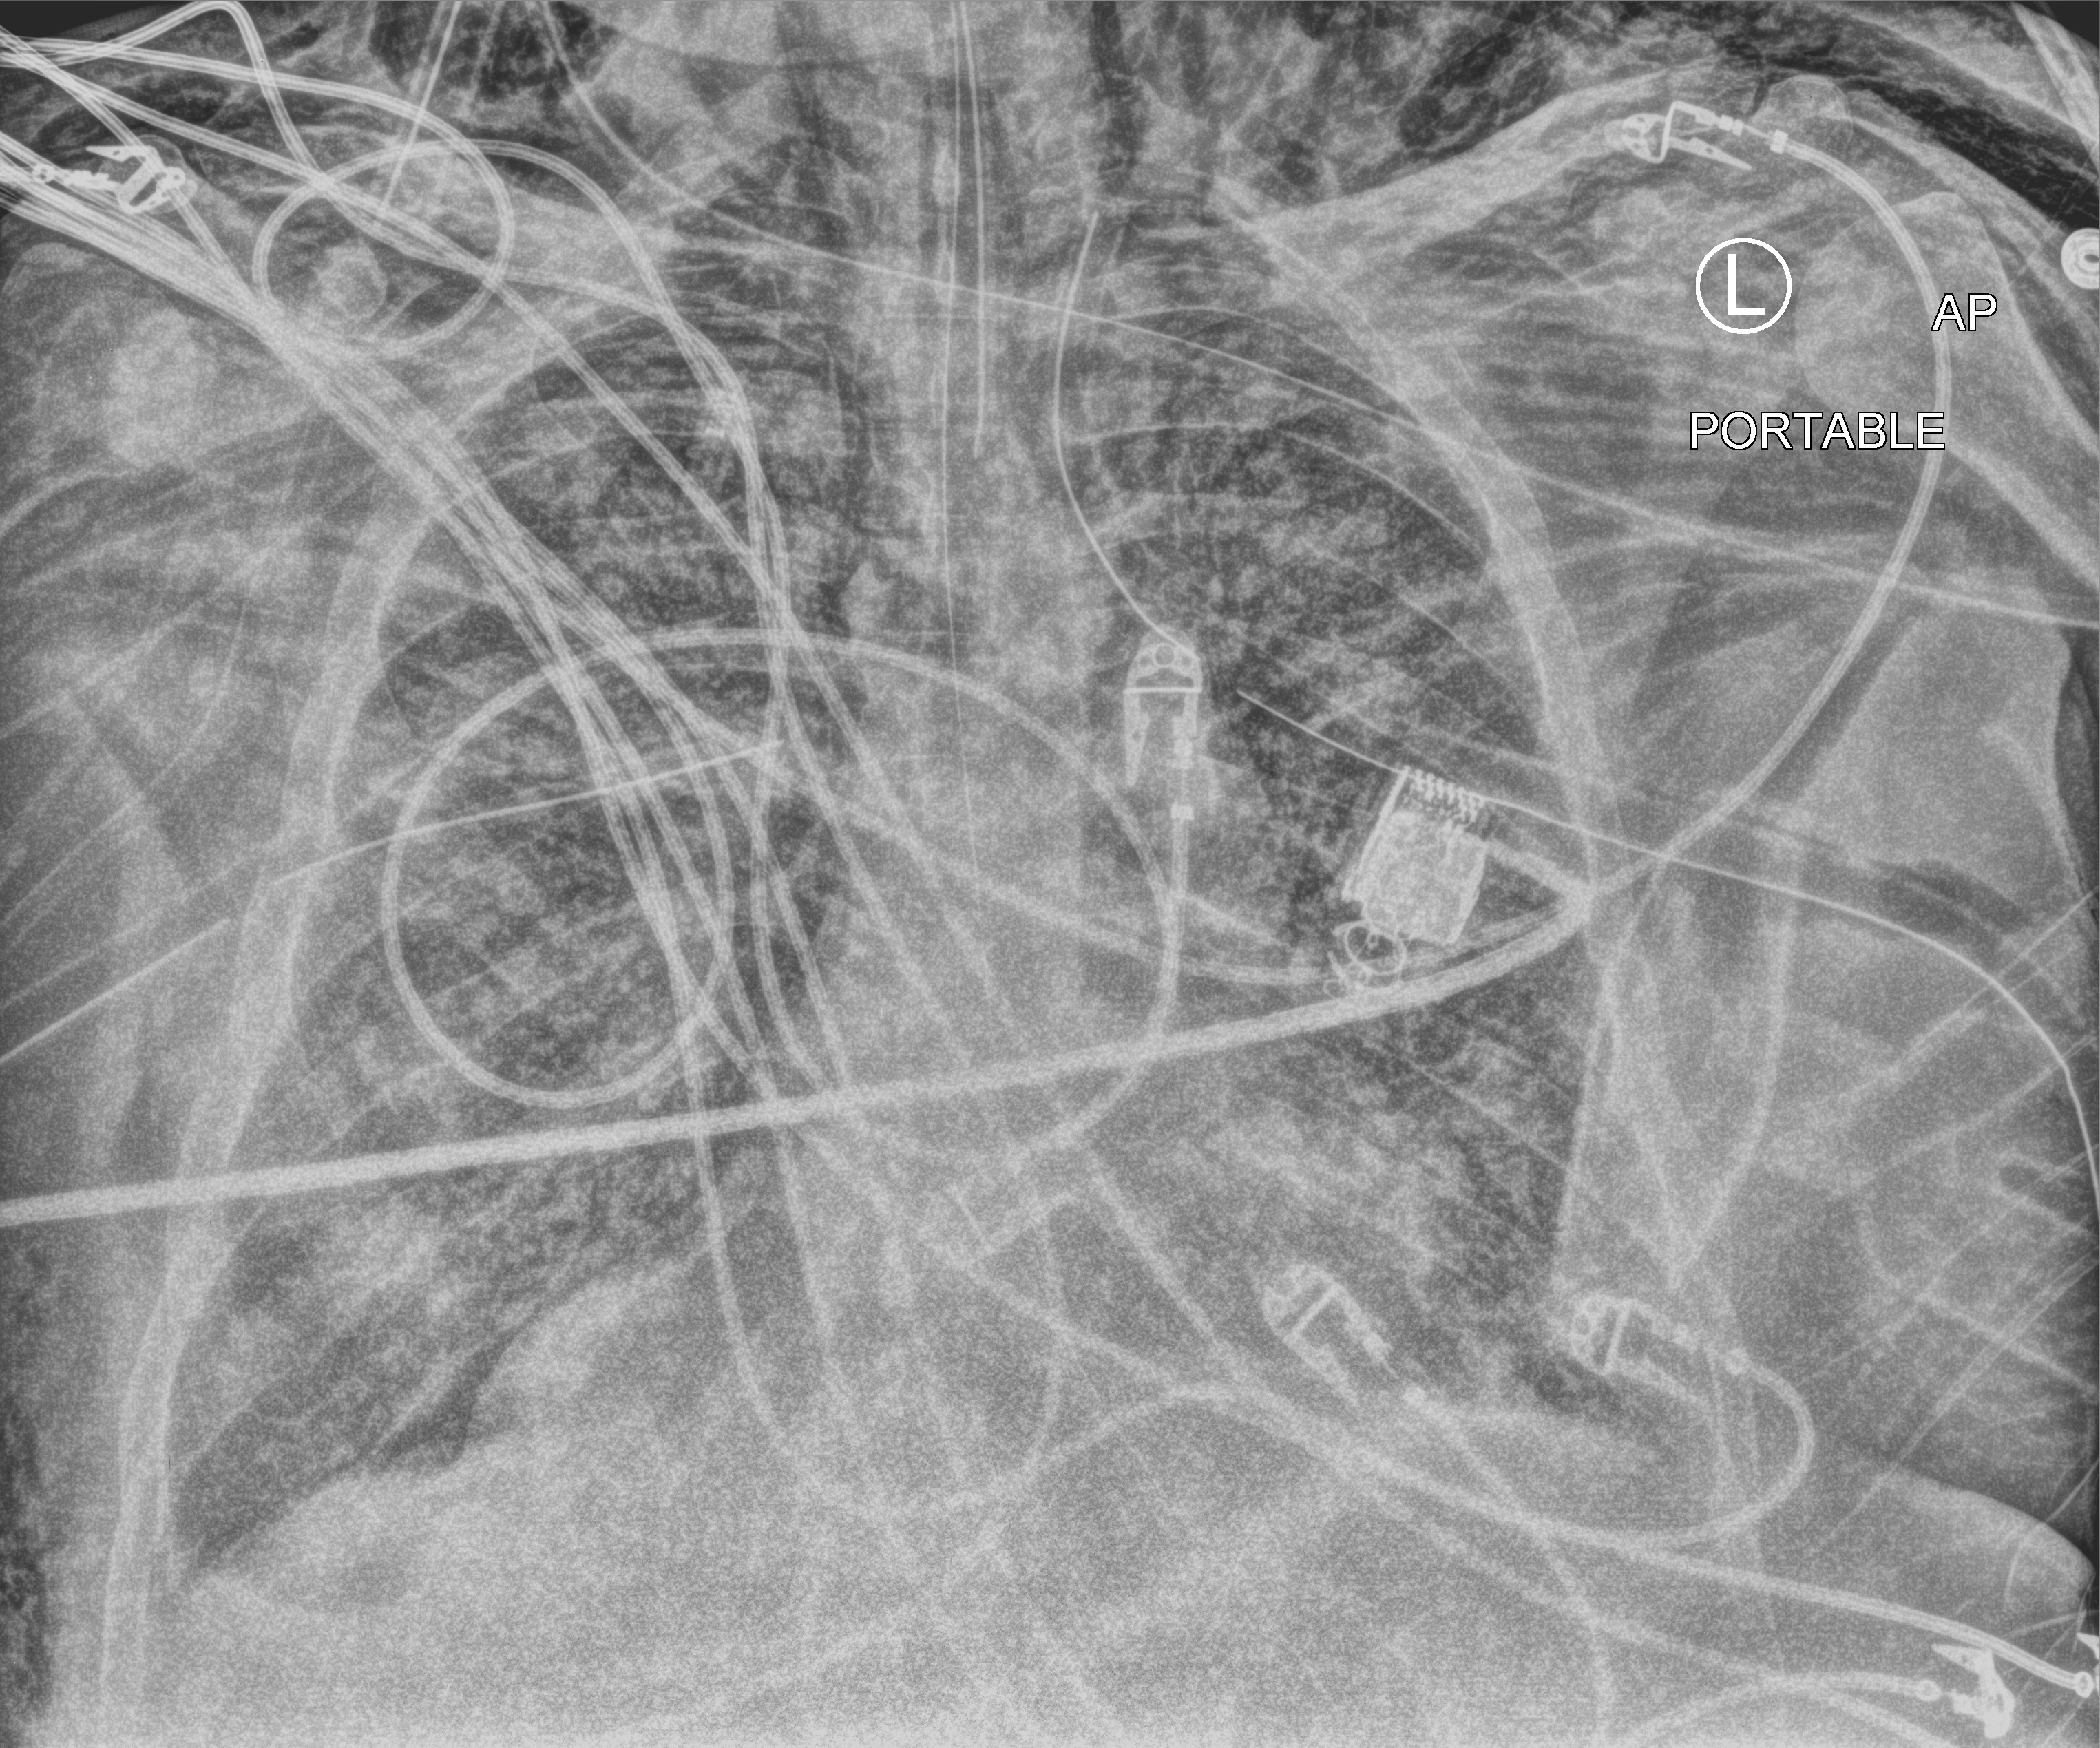
Portable chest radiograph; anteroposterior (AP) projection. Patient hospitalised with COVID-19, aged 18–59 years.
Hospital-stay facts (about this admission, not read from this image; timing relative to this image not recorded): chronic kidney disease (admission record): no.